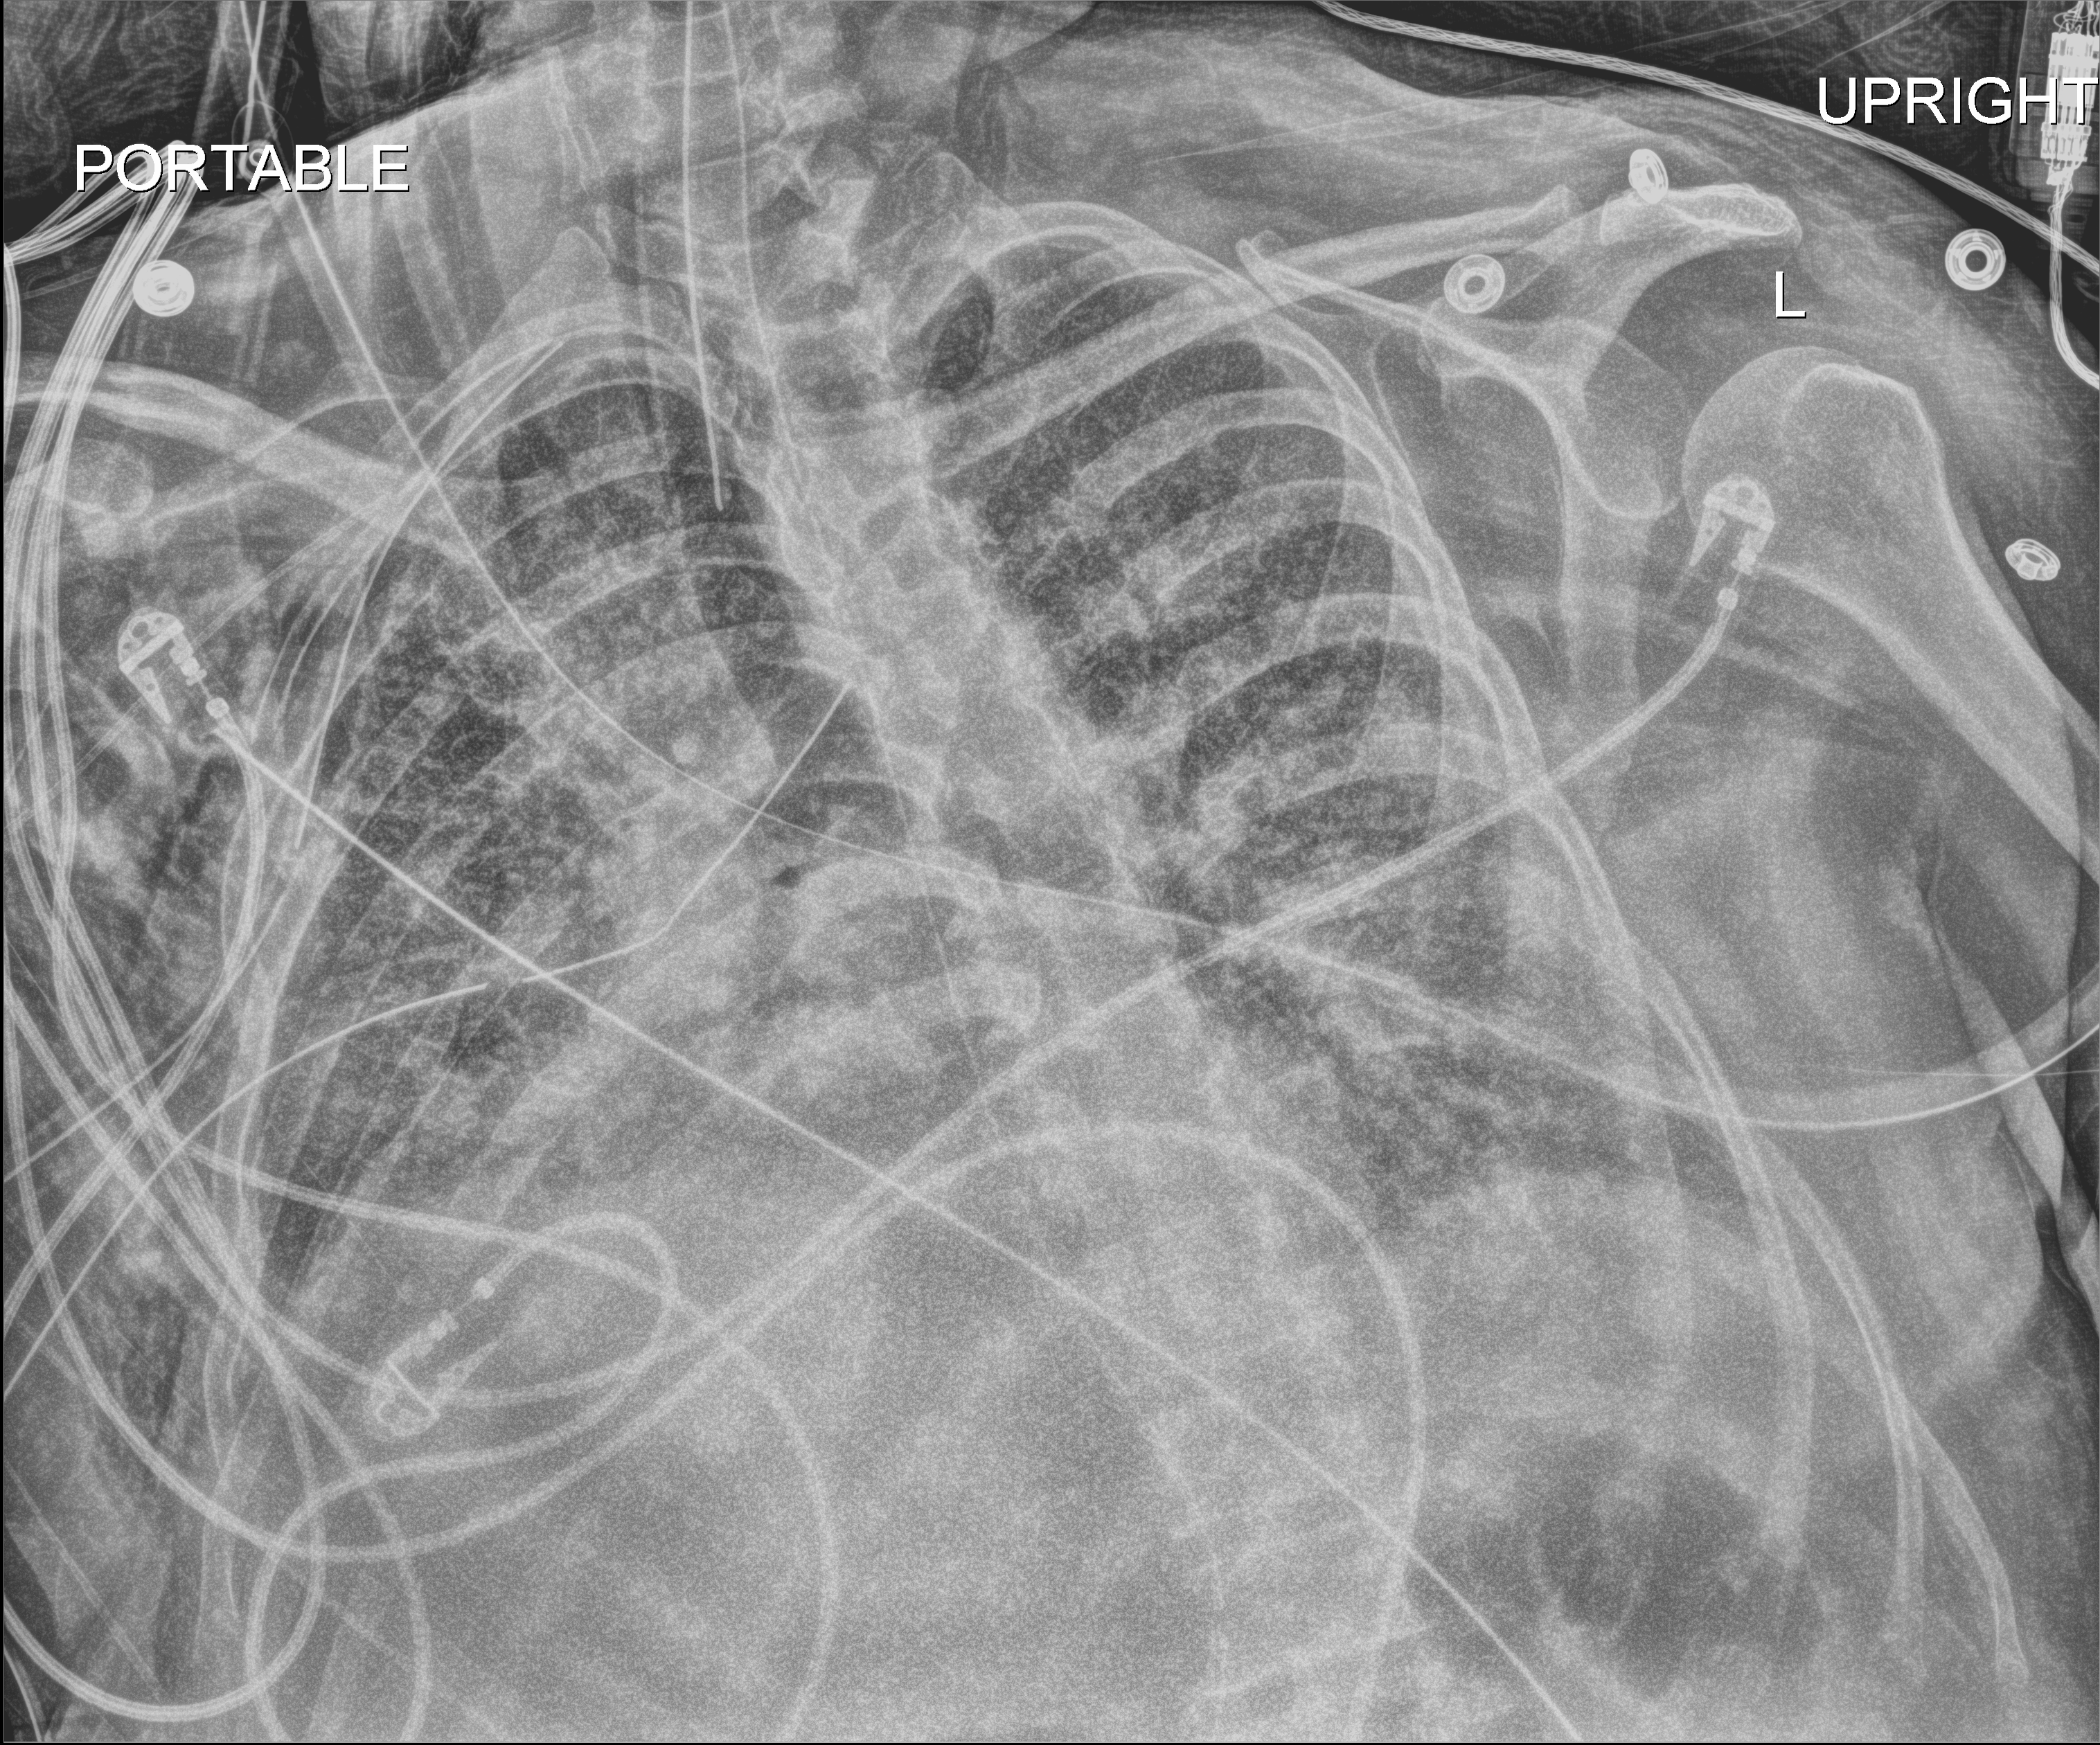
Chest X-ray (portable), anteroposterior (AP) projection. Patient hospitalised with COVID-19, aged 18–59 years.
Admission-level facts for this patient (not findings on this image; timing relative to this image not recorded):
- diabetes (admission record): no
- mechanically ventilated during this hospital stay: yes
- hypertension (admission record): no